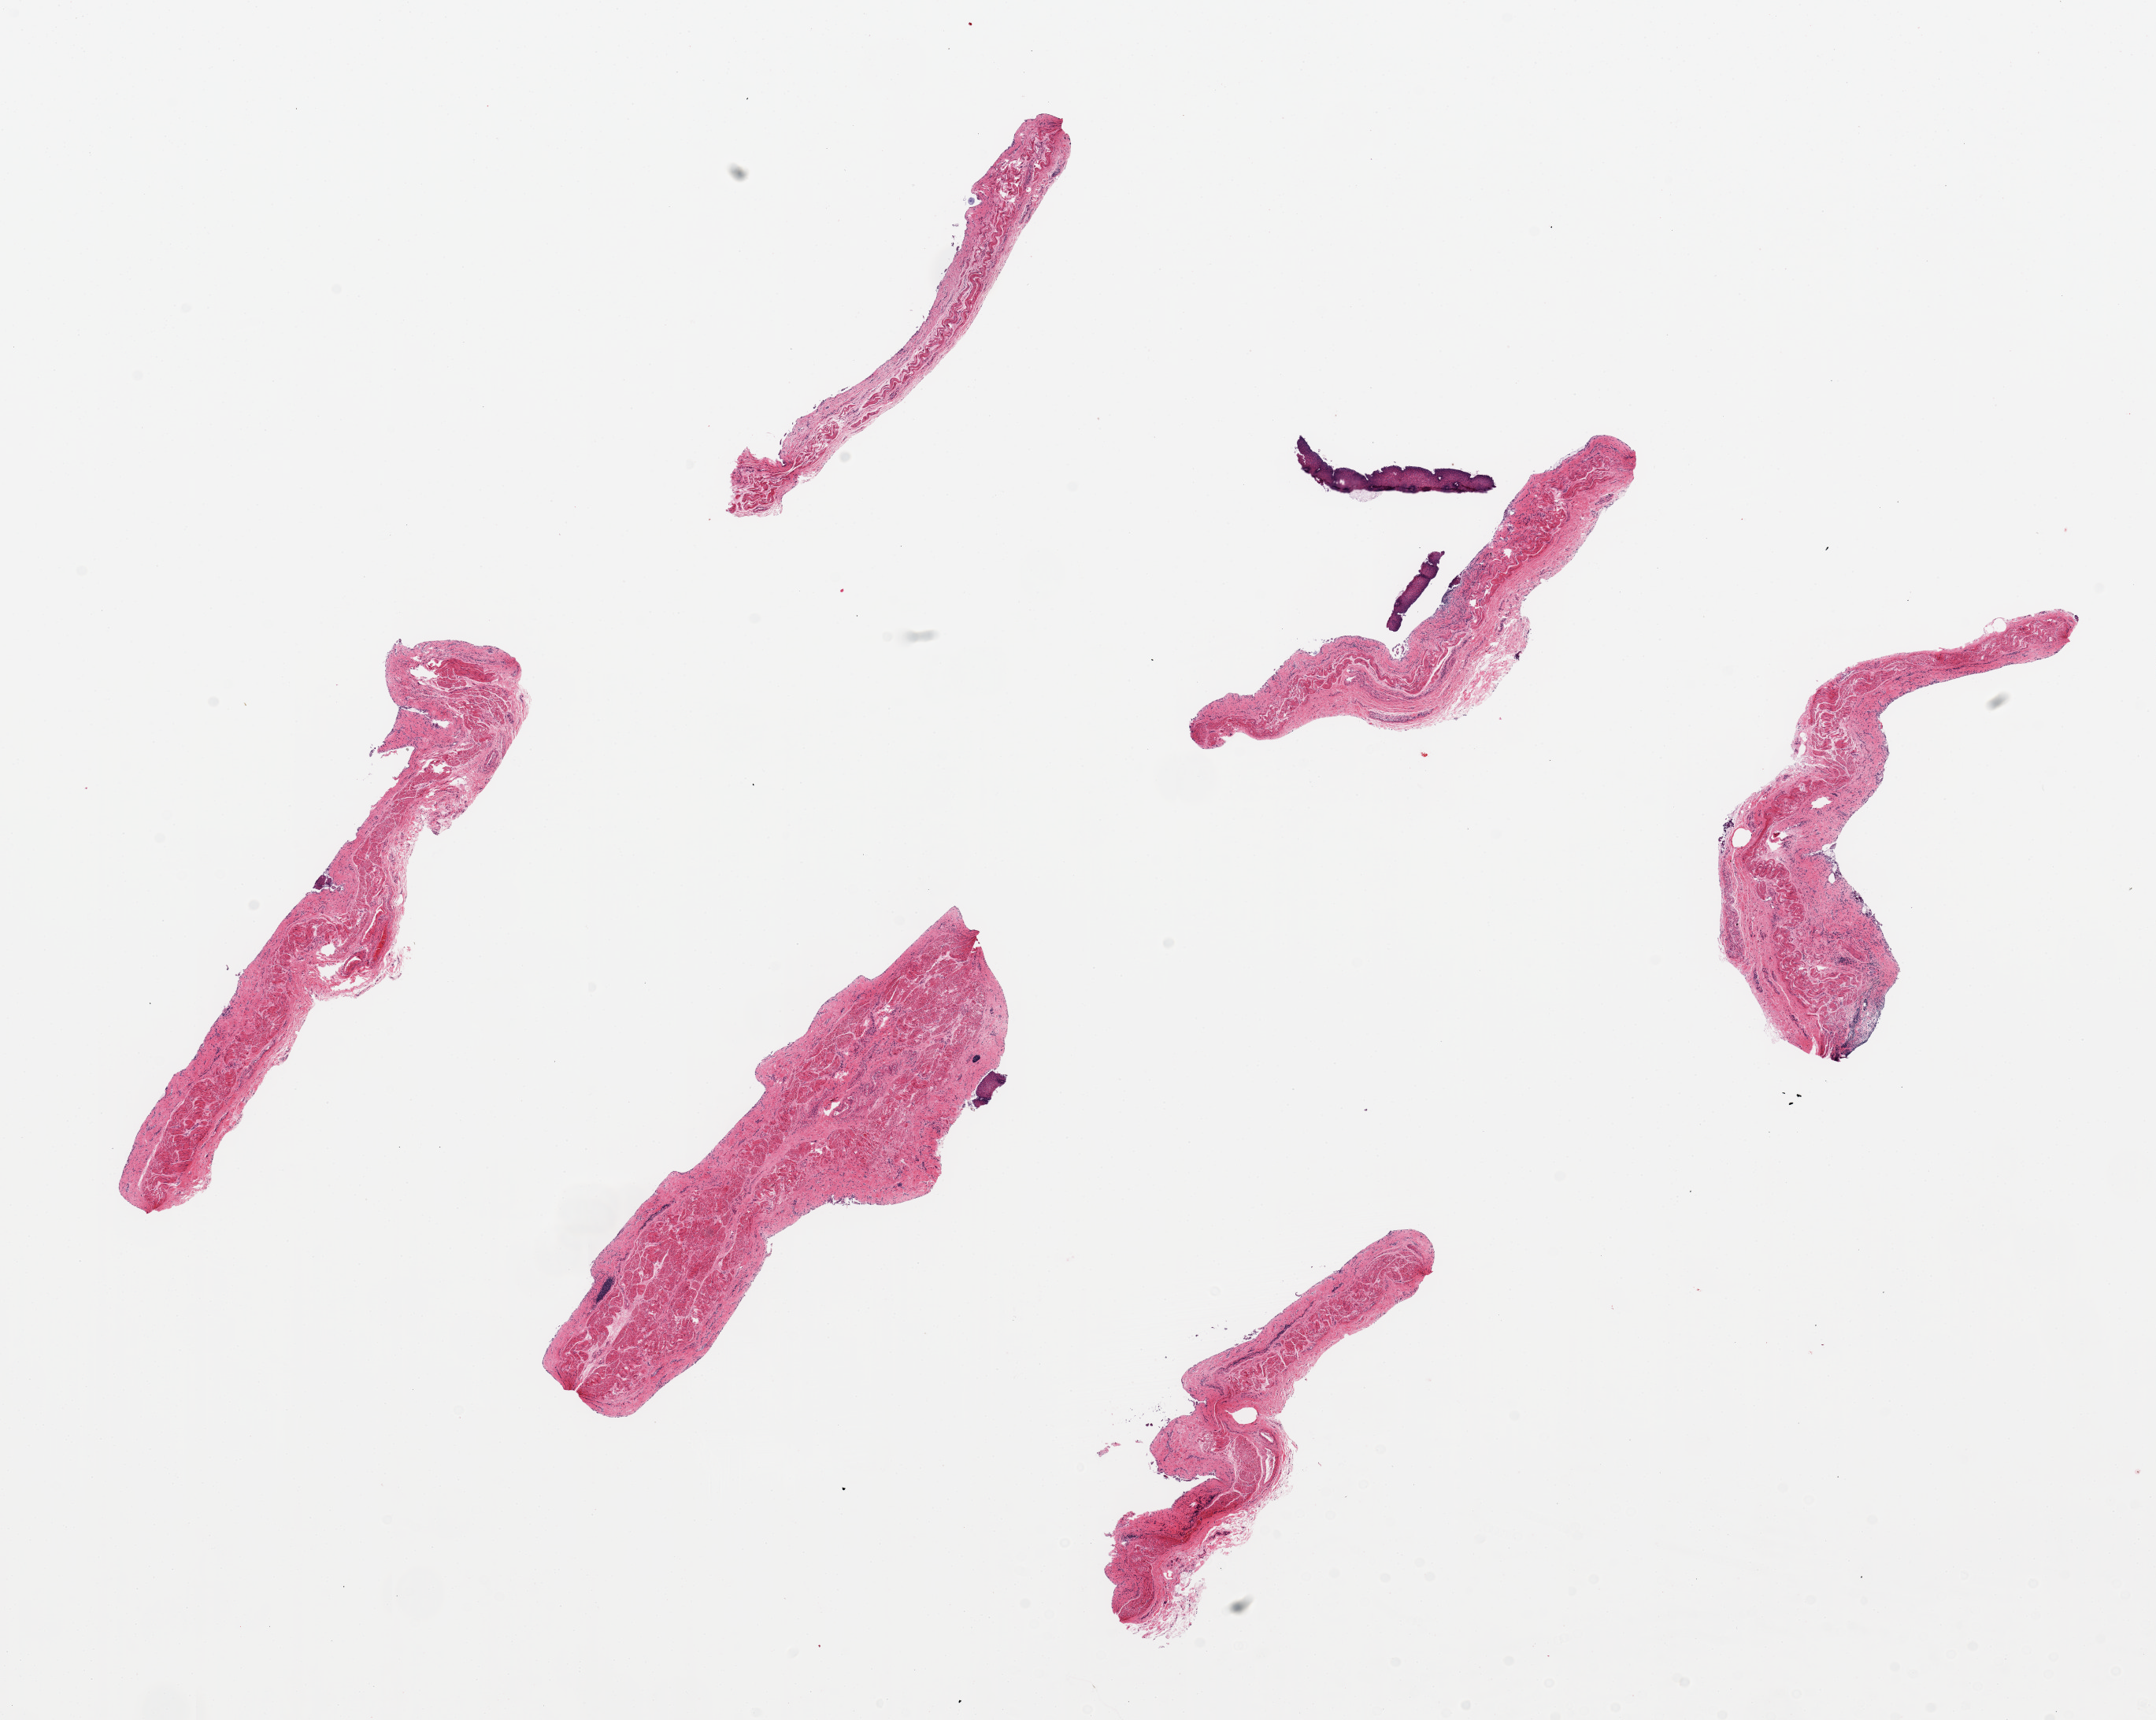
Digitized hematoxylin and eosin (H&E)-stained section, brightfield, whole scanned area (about 21.7 x 17.3 mm) shown as a low-resolution overview, PAXgene-fixed, paraffin-embedded tissue, sampled site (target tissue): esophageal mucous membrane, donor tissue sample. Donor sex: male.
Reviewer comment on this tissue sample: 6 pieces, singlue minute fragment of squamou mucosa; rest is fibrous tissue.